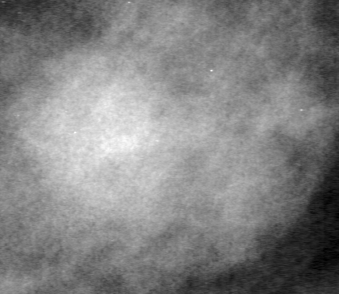
Cropped region of a digitized screen-film mammogram centred on a radiologist-marked abnormality; left breast; CC view.
- Mass, shape round, margins ill defined; BI-RADS assessment category 4; subtlety rating 3 on a 1 (subtle) to 5 (obvious) scale; pathology result (as recorded, not read from the image): malignant.